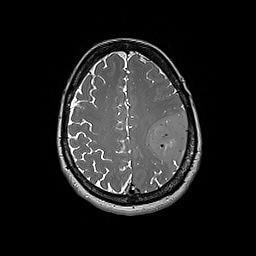
Brain MRI from a brain-tumour surgery series, one axial slice; position 65 of 192 along the scan axis; 1 mm slice thickness; 256 × 256 image matrix. From the clinical record (not read from this slice): histopathology: Glioblastoma; WHO grade: 4; IDH mutation: no.
Structures marked on this image (outlined manually by an expert reader):
- tumour: bounding box [x1, y1, x2, y2] px = [149, 114, 189, 164]